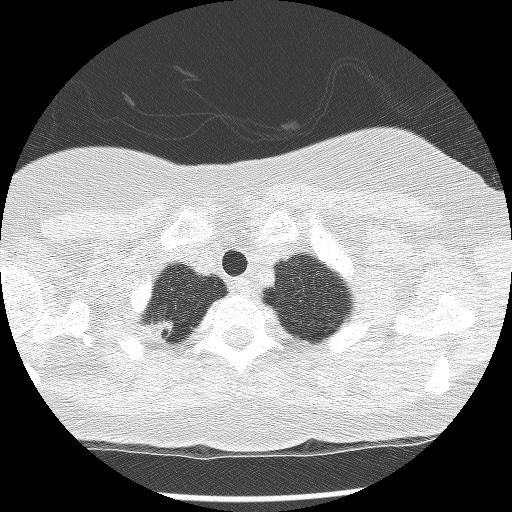
Chest CT (low-dose screening protocol), one axial image, second screening round (one year after baseline), lung window (W 1500 / L -600 HU), lung (sharp) reconstruction kernel (BONE). Female participant, aged 56 years at enrolment. Current smoker at enrolment.
Expert-annotated lung lesion, box from (x=136, y=307) to (x=186, y=355) px. Screening reader's record for this exam: no non-calcified nodule ≥4 mm recorded. Lung cancer was diagnosed 366 days after this screen: large cell carcinoma, NOS, right upper lobe, poorly differentiated (G3), stage IB (AJCC 6th edition), 15 mm at pathology.